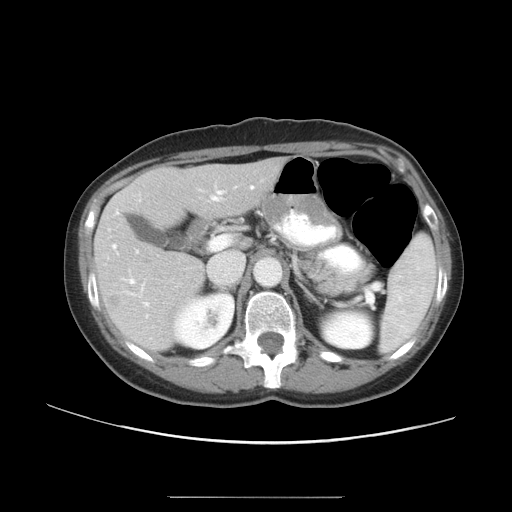
Contrast-enhanced abdominal CT, one axial slice. Slice 28 of 50 in the series (ordered by position). 120 kVp. Intravenous contrast given. Soft-tissue window (W 400 / L 40 HU). 5 mm slice thickness. 512 × 512 image matrix. Female patient, age 58 years. From the clinical record (not read from this slice): diagnosis: colorectal cancer liver metastases, imaged before liver resection; multiple liver metastases: yes; largest metastasis: 7.3 cm; disease in both lobes: yes.
Annotated regions visible in this slice (outlined manually by an expert reader):
- hepatic veins: bounding box (x1, y1, x2, y2) in pixels: (113, 186, 254, 253)
- liver: (96, 160, 282, 351)
- planned liver remnant (the part of the liver to remain after resection): (169, 160, 282, 219)
- portal vein (with intrahepatic branches): (129, 191, 222, 306)
- liver metastasis: (111, 296, 121, 310)